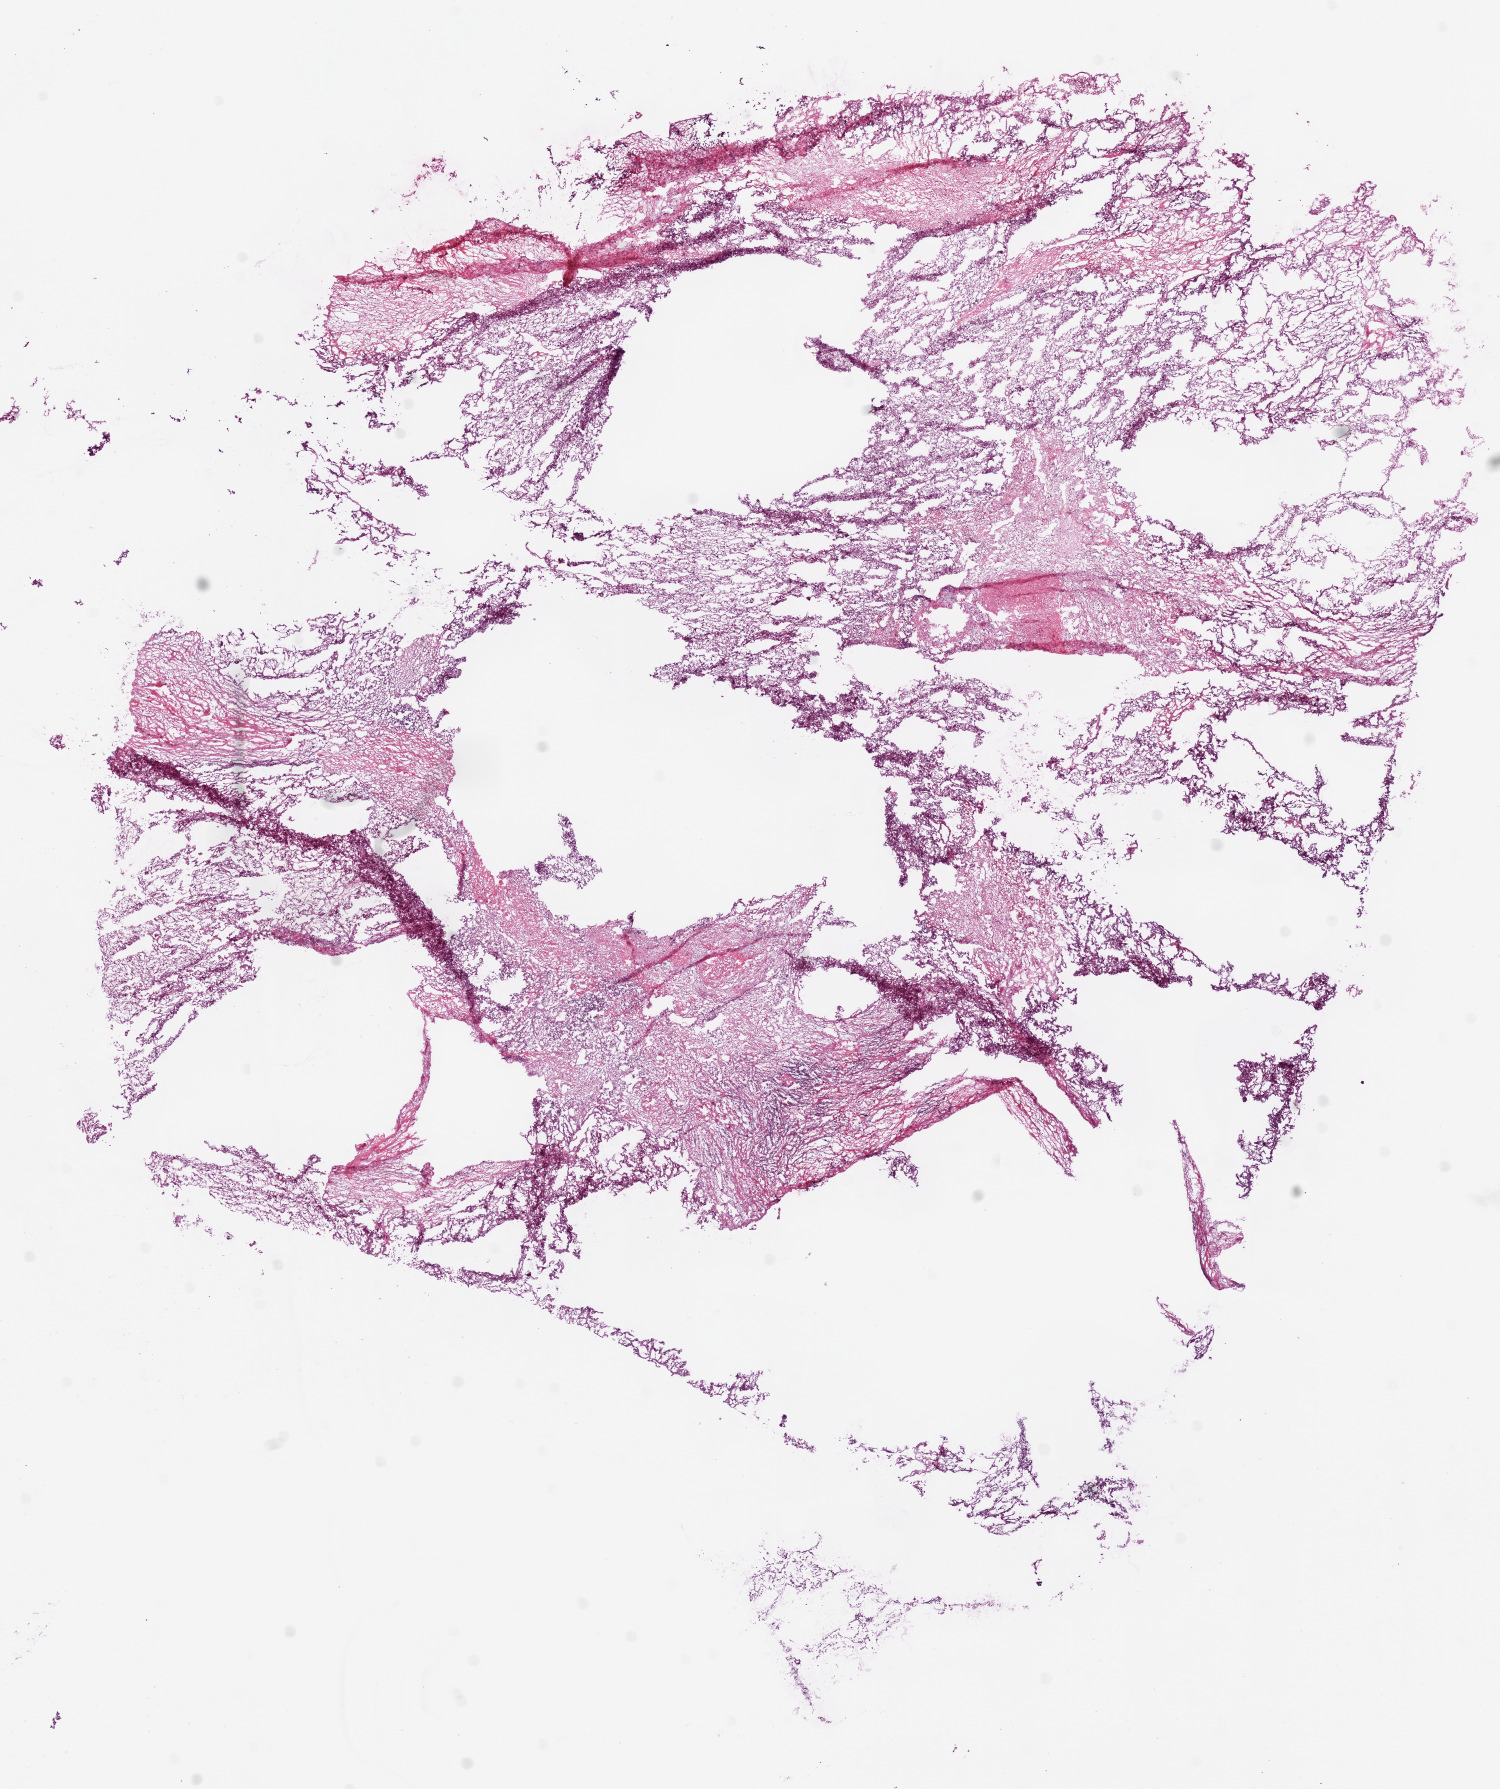
Whole-slide histology image, Hematoxylin and eosin (H&E) stained — low-resolution overview of the scanned area, about 12.0 x 14.4 mm; frozen section; primary tumour sample from the kidney. Patient: male, age at initial diagnosis 59 years. Histologic grade: G2 (moderately differentiated). Pathologist review of this section (percent, as recorded): tumour cells 82%, tumour nuclei 85%, normal cells 0%, stromal cells 18%, necrosis 0%.
Laterality: right. Histologic diagnosis: Clear cell adenocarcinoma, NOS. AJCC pathologic stage: III.